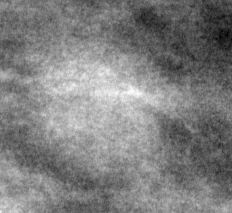
Cropped region of a digitized screen-film mammogram centred on a radiologist-marked abnormality; right breast; MLO view; BI-RADS breast density category 1 (scale 1–4).
Finding: mass, shape irregular, margins ill defined; BI-RADS assessment category 4; pathology result (as recorded, not read from the image): malignant.